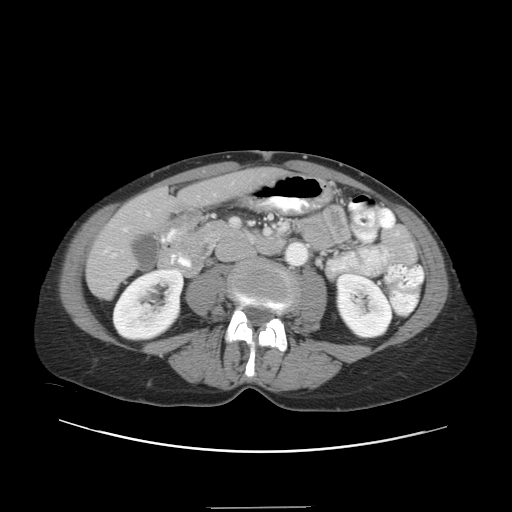
Contrast-enhanced abdominal CT, one axial slice; slice 9 of 38 in the series (ordered by position); reconstruction kernel STANDARD; 120 kVp; intravenous contrast given; soft-tissue window (W 400 / L 40 HU); 5 mm slice thickness; 512 × 512 image matrix, field of view 388 × 388 mm. Female patient, age 64 years. Case-level facts recorded for this patient, not image findings: diagnosis: colorectal cancer liver metastases, imaged before liver resection; multiple liver metastases: no; largest metastasis: 3.8 cm; disease in both lobes: yes.
Annotated regions visible in this slice (outlined manually by an expert reader):
- hepatic veins: bounding box <123,194,216,232> (left, top, right, bottom; pixels)
- liver: <88,170,277,297>
- planned liver remnant (the part of the liver to remain after resection): <173,170,277,207>
- portal vein (with intrahepatic branches): <111,253,116,257>